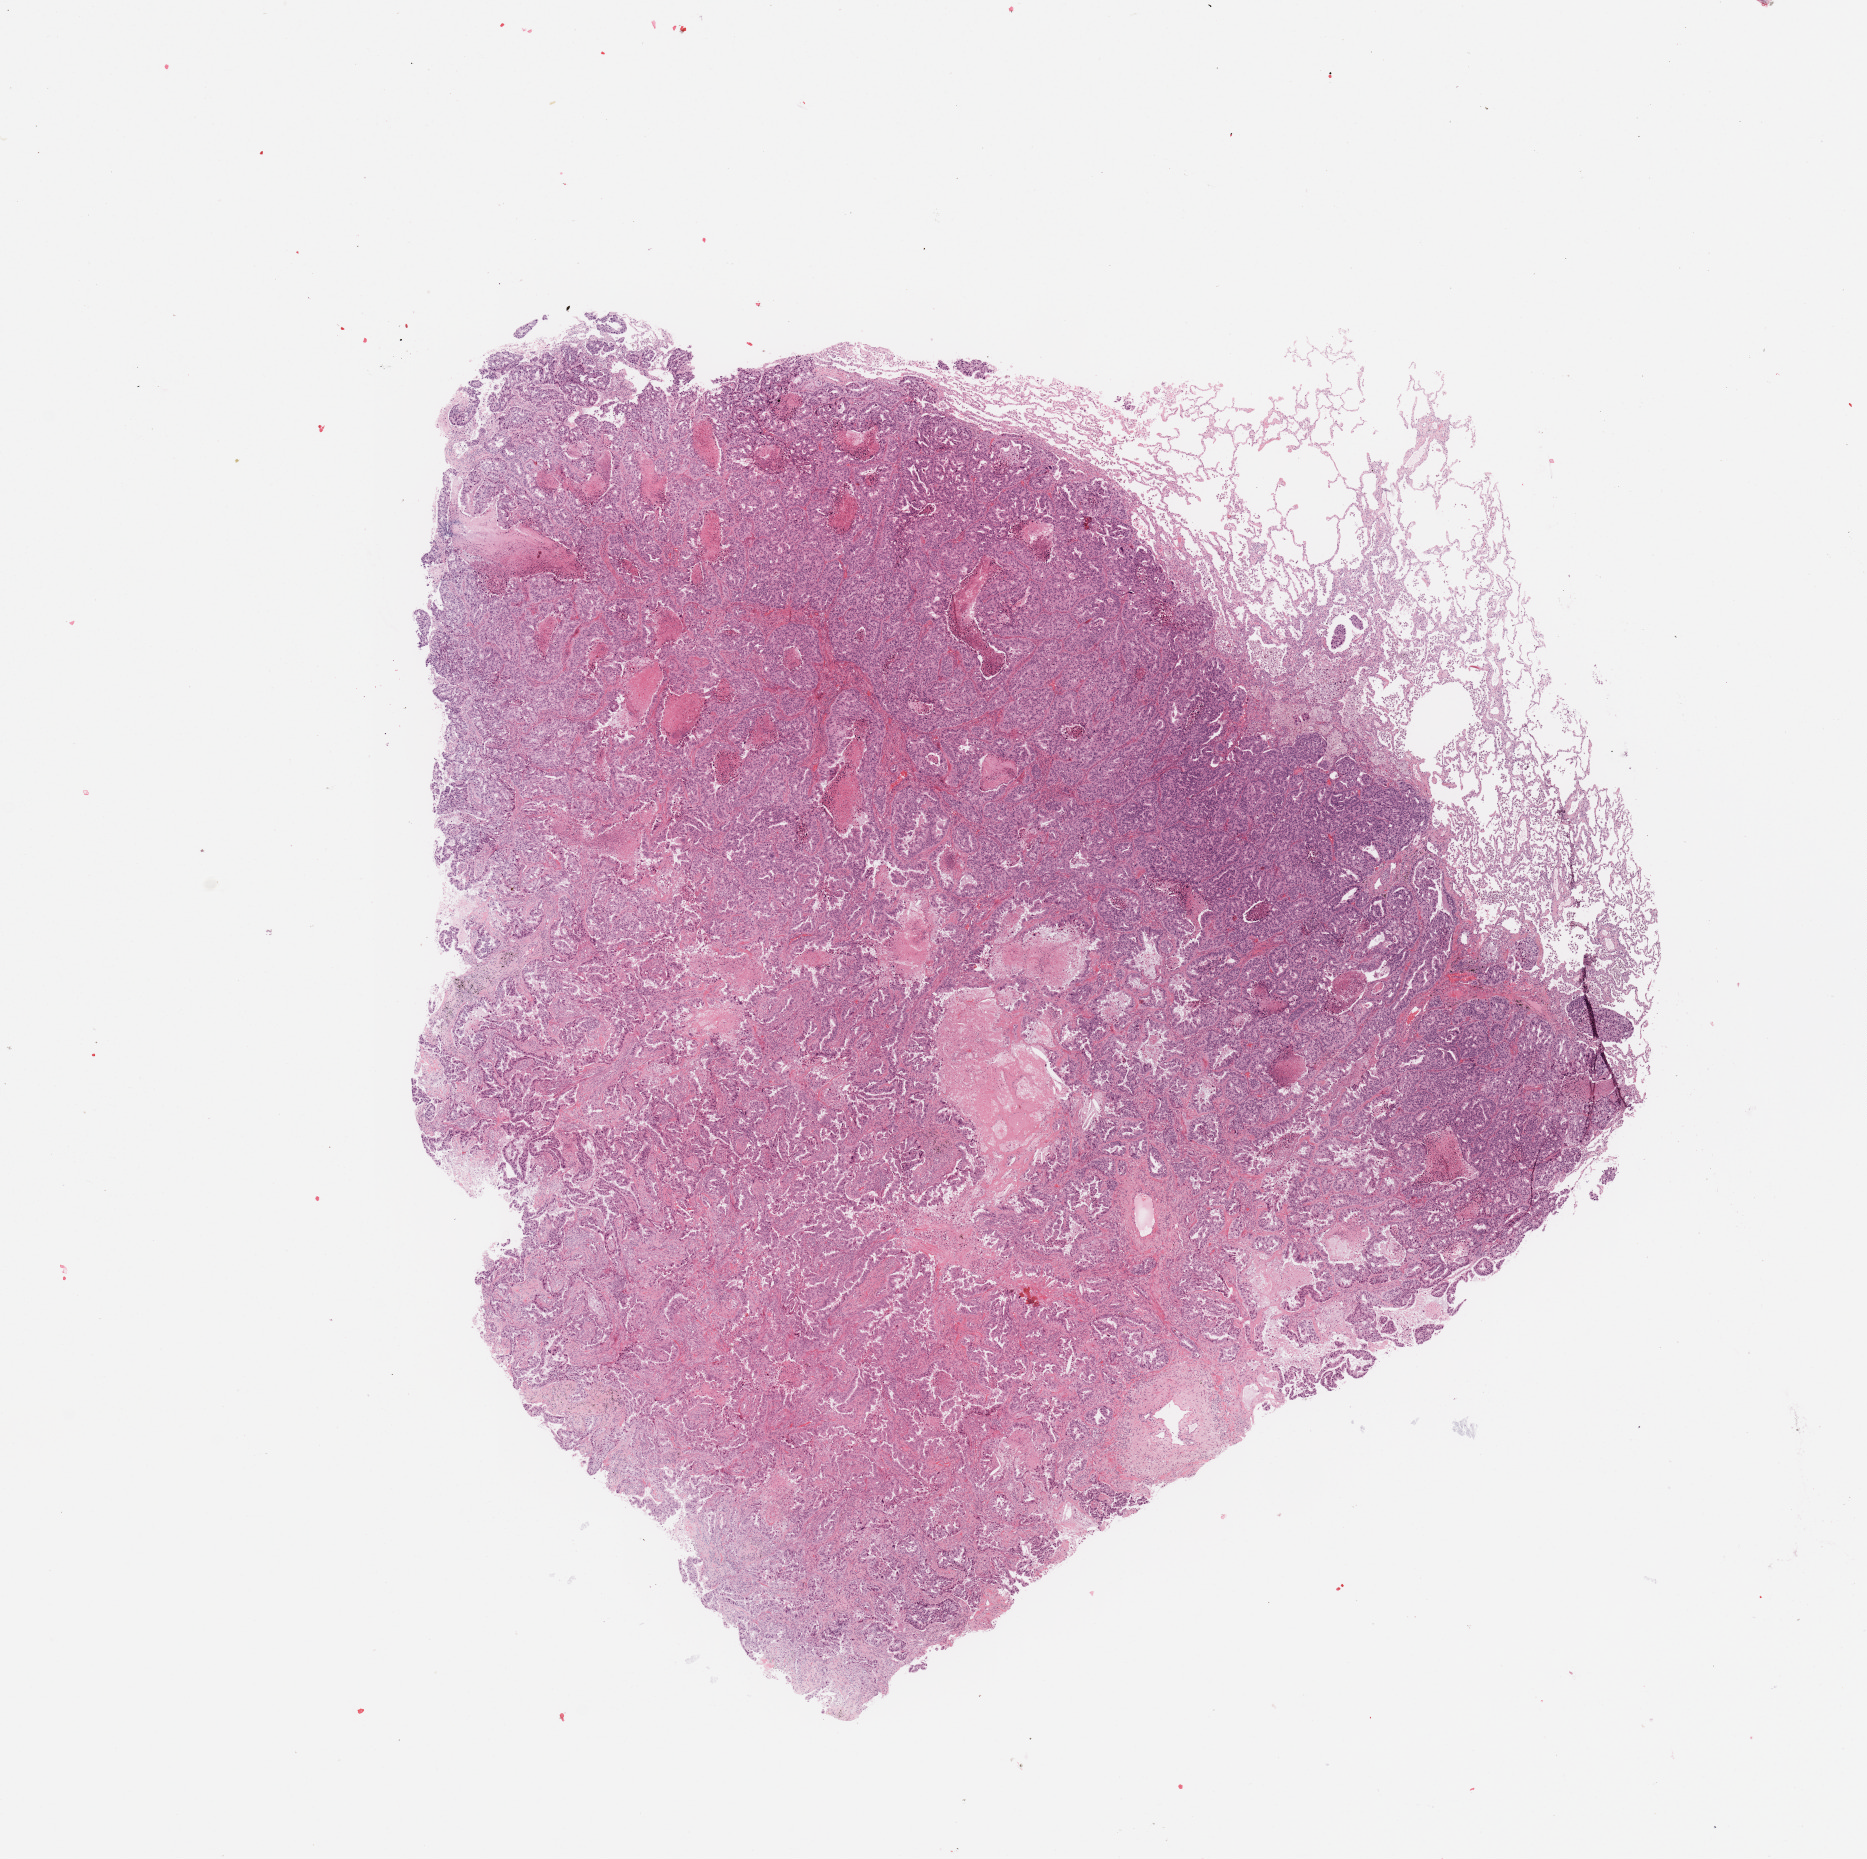
Digitized H&E tissue section (whole slide) — low-resolution overview of the scanned area, about 14.8 x 14.7 mm, tumour tissue sample, sampled site: lung. Patient: male, age 62 years. Histologic grade: G2 (moderately differentiated). Slide review estimates, as recorded: tumour nuclei 80%, necrosis 5%.
* histologic diagnosis: Adenocarcinoma, NOS
* AJCC pathologic stage: IIB